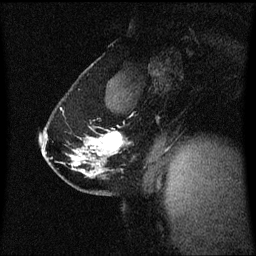
Breast MRI (dynamic contrast-enhanced), one sagittal slice; position 40 of 60 along the scan axis; dynamic contrast-enhanced series, image 2 of 3 at this slice position (ordered by acquisition); 1.5 T; TE 4.2 ms, TR 8.4 ms; 256 × 256 image matrix, field of view 210 × 210 mm. Female patient, age 40 years. From the clinical record (not read from this slice): setting: breast cancer imaged before/during neoadjuvant chemotherapy; receptor status: triple-negative.
Structures marked on this image (semi-automatically segmented with operator editing):
- analysis volume of interest (the breast-tissue region the enhancement analysis was run in; not a lesion): bounding box <40,123,126,186> (left, top, right, bottom; pixels)
- tumour enhancement mask (voxels above the 70 % enhancement threshold inside the analysis volume of interest): <77,134,123,161>